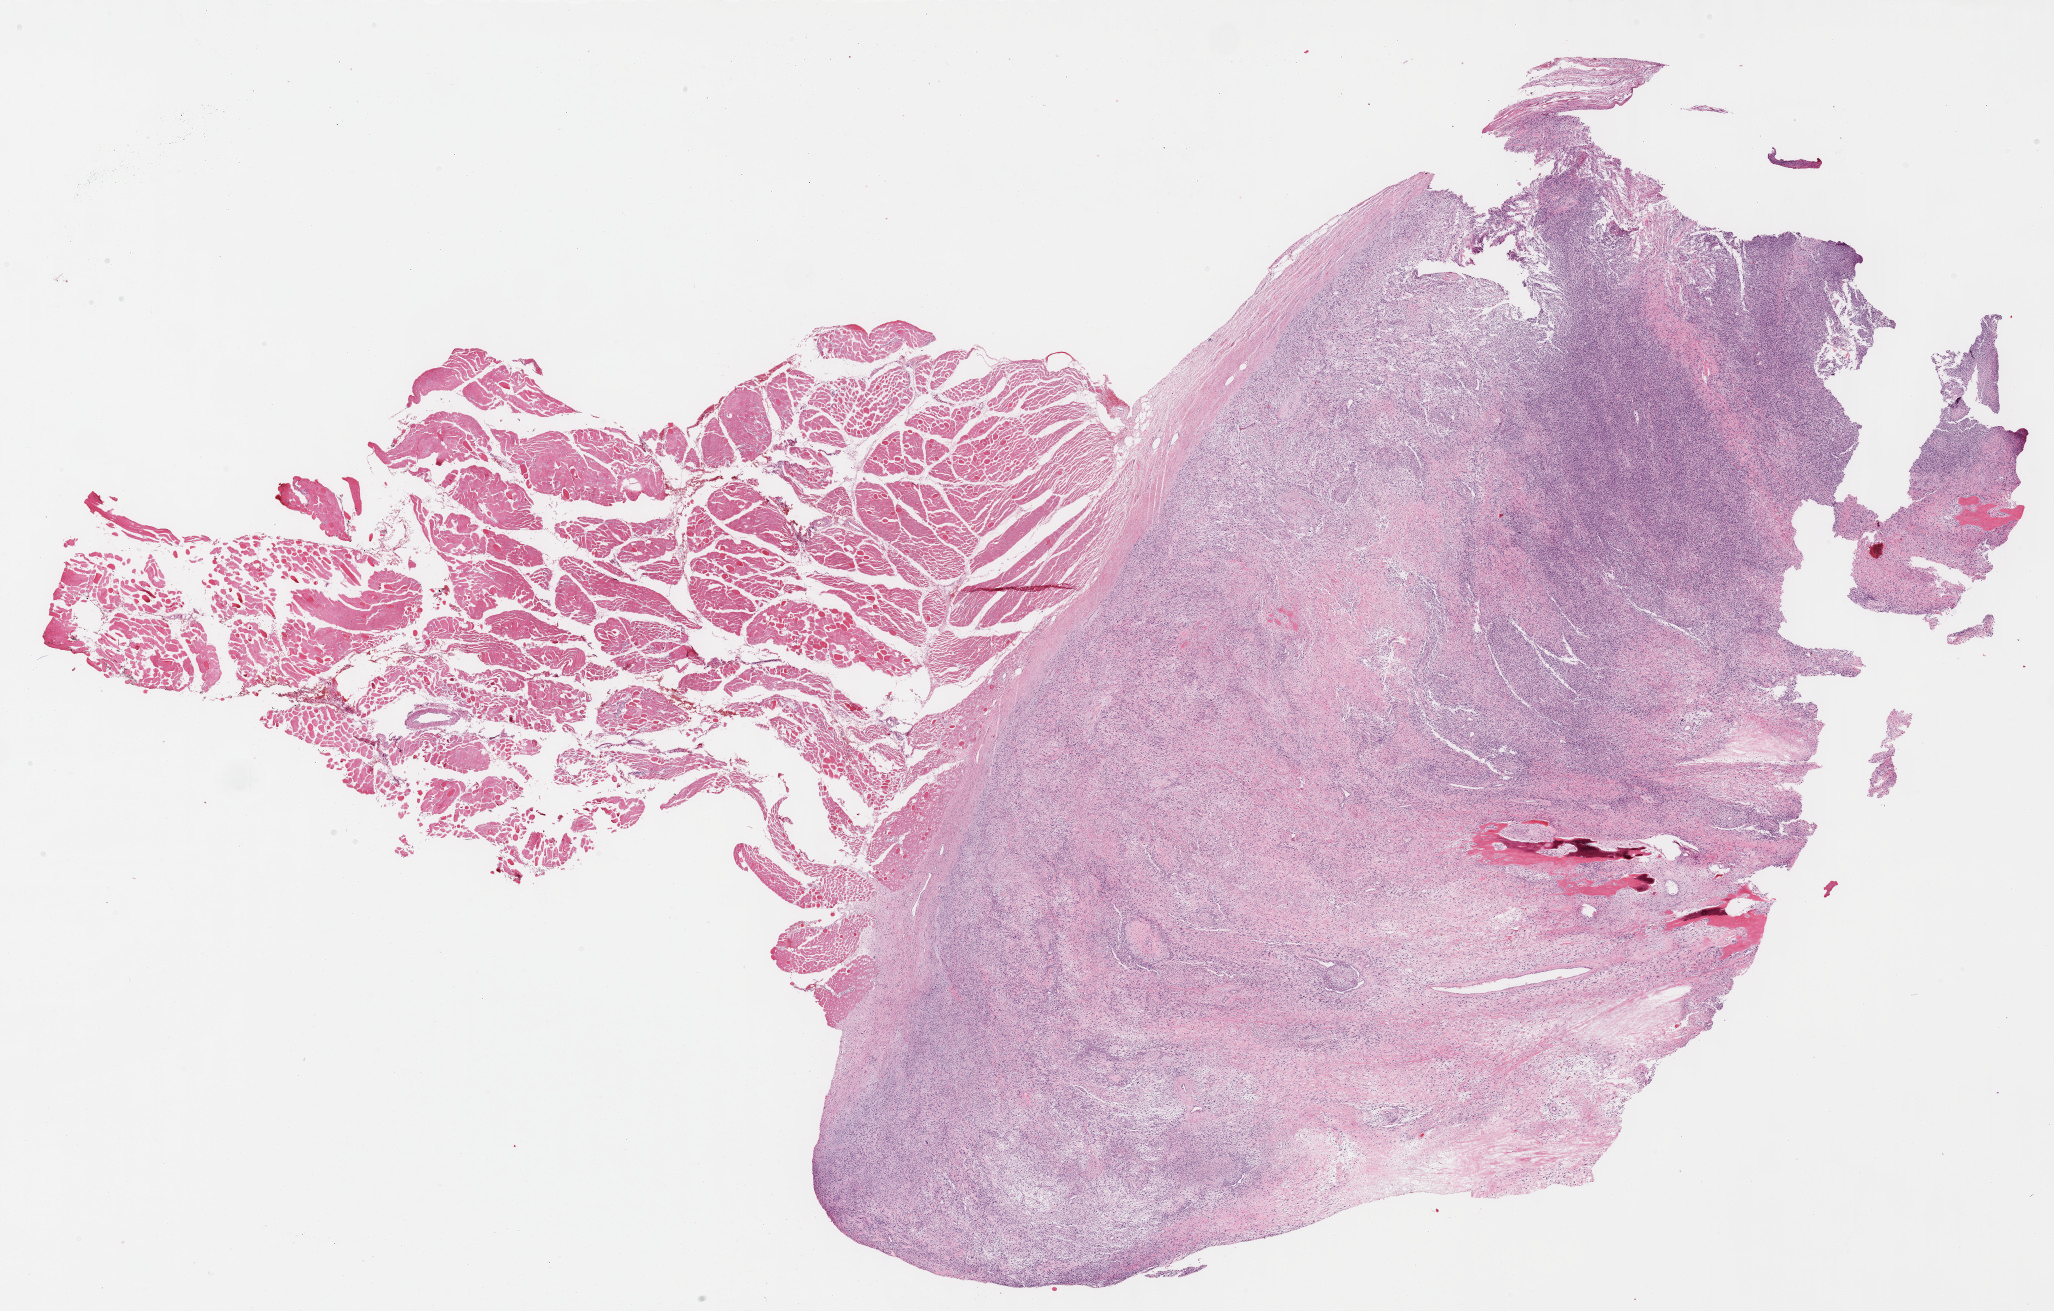
Whole-slide histology image, H&E-stained — whole scanned area (about 33.2 x 21.2 mm, slide scanned at 40x) shown as a low-resolution overview; FFPE section; sample: primary tumour, retroperitoneum and peritoneum. Male patient; age at initial diagnosis 72 years.
Diagnosis: Sarcoma, NOS (retroperitoneum).